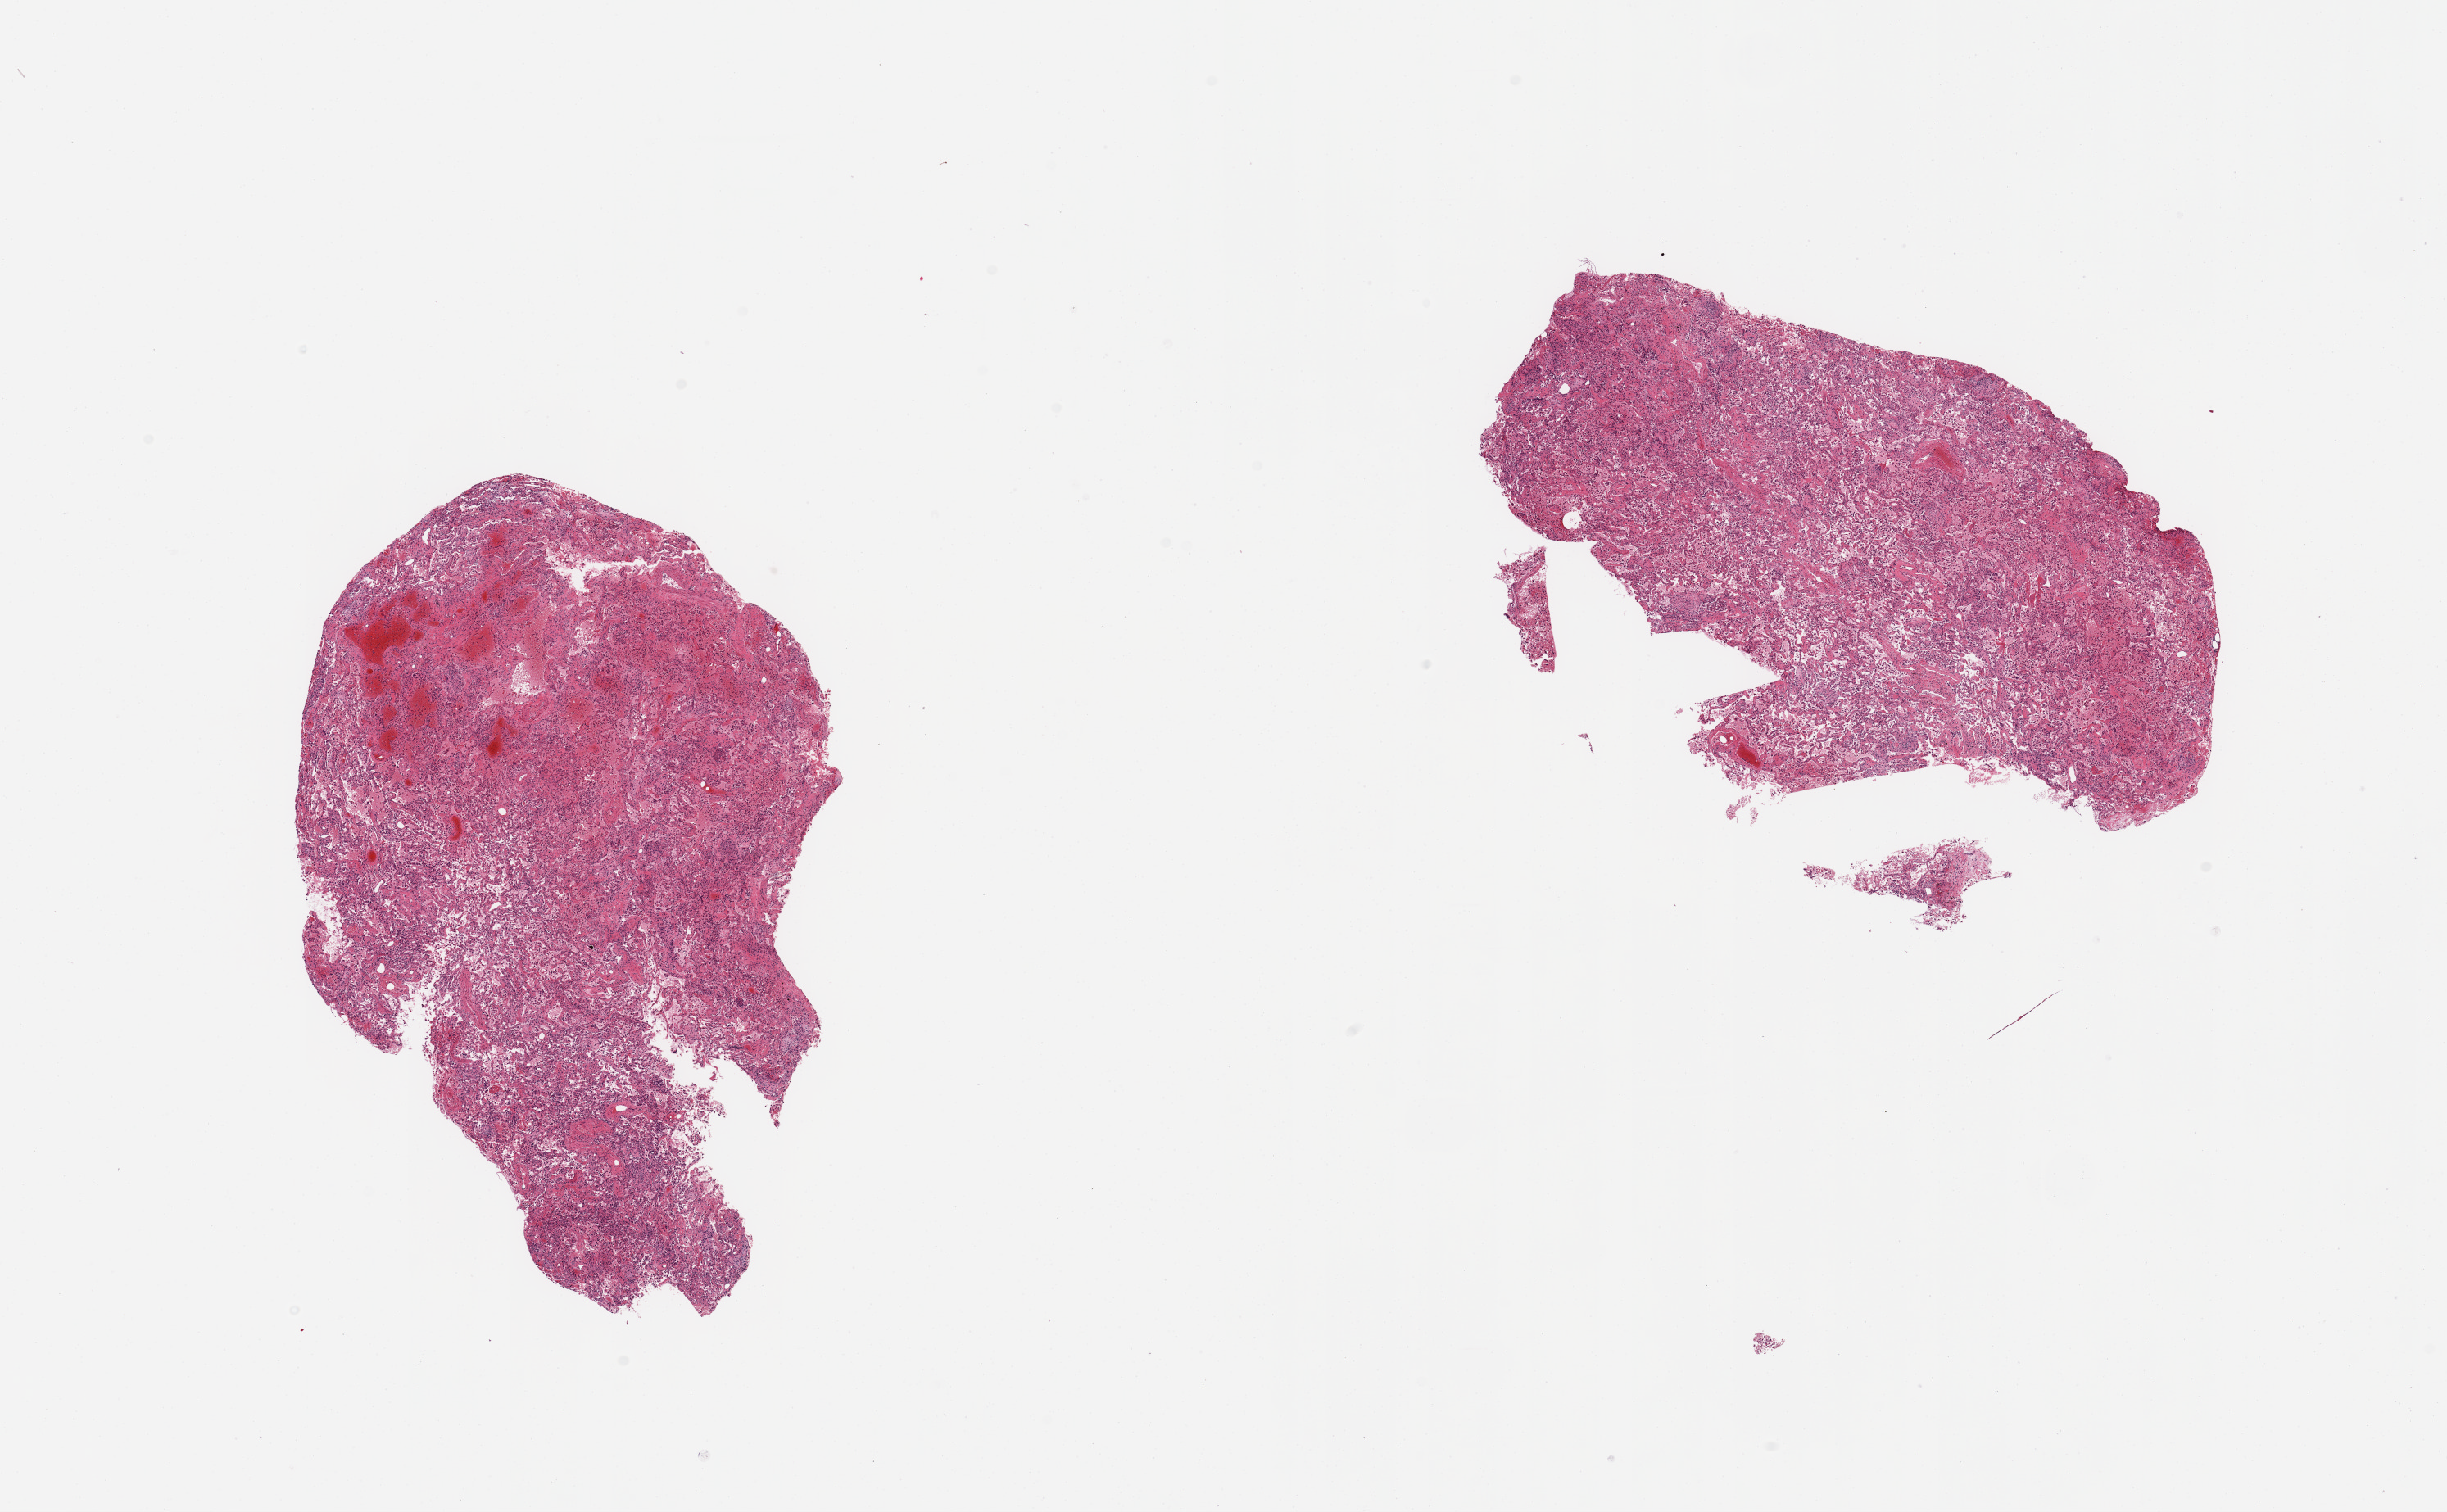
Digitized hematoxylin and eosin (H&E)-stained section, whole scanned area (about 23.6 x 14.6 mm, acquisition: 20x scan) shown as a low-resolution overview; PAXgene-fixed paraffin-embedded (PFPE) section; section of lung (target tissue); donor tissue sample. Male donor.
Review note (as recorded): 2 pieces; alveolar hemorrhage, macrophages and fibrosis.